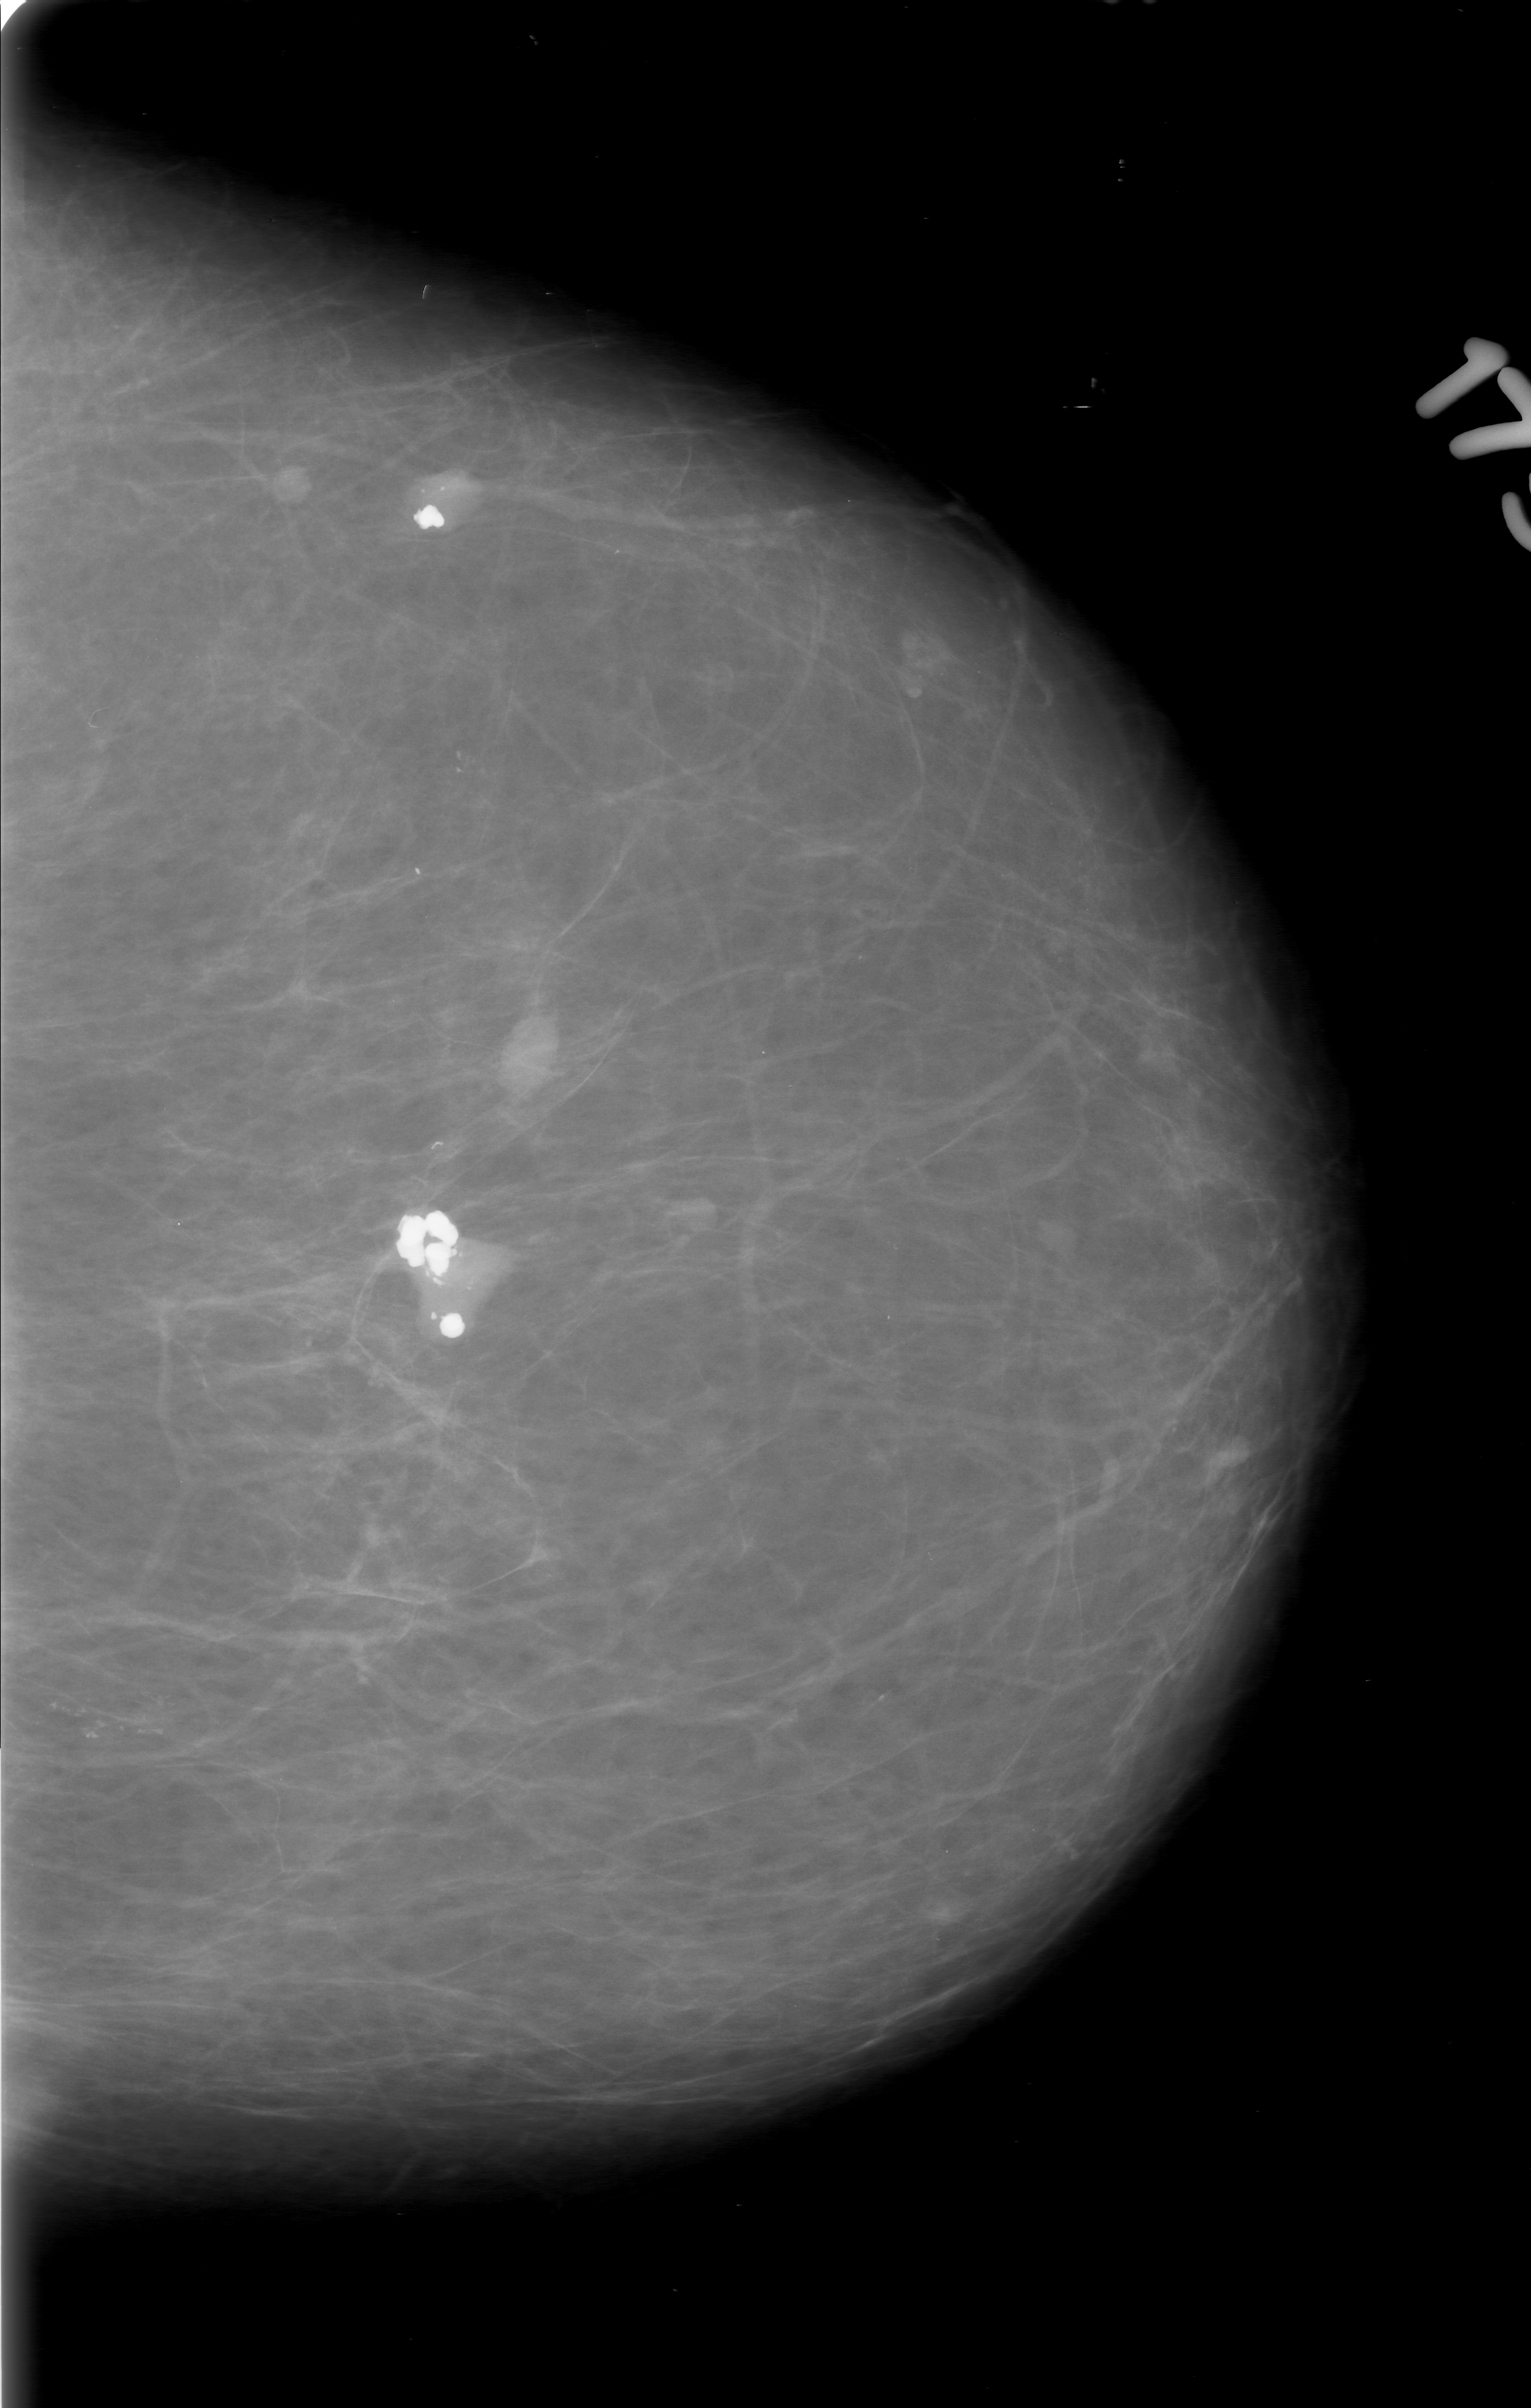
Scanned film-screen mammogram; left breast; CC view.
Calcifications, morphology pleomorphic, distribution segmental; BI-RADS assessment category 0; pathology (as recorded): benign.